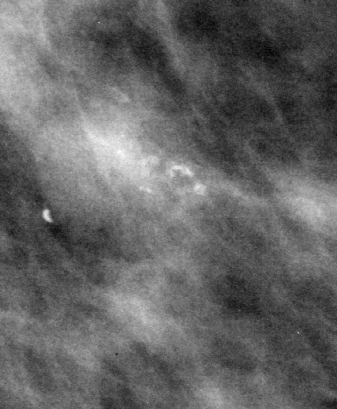
Cropped region of a digitized screen-film mammogram centred on a radiologist-marked abnormality, left breast, MLO view, BI-RADS breast density category 3 (scale 1–4).
- Calcifications, morphology amorphous, distribution clustered; BI-RADS assessment category 4; pathology (as recorded): benign.